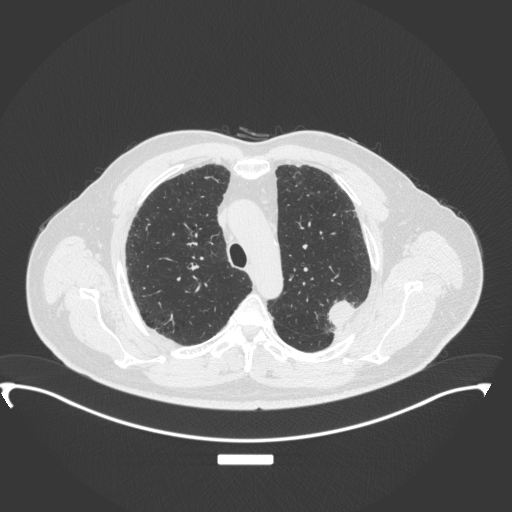
Chest CT, one axial slice; slice 269 of 350 in the series (ordered by position); 120 kVp; lung window (W 1500 / L -600 HU); 1 mm slice thickness; 512 × 512 image matrix, field of view 459 × 459 mm. Male patient, age 64 years. From the clinical record (not read from this slice): clinical TNM (as recorded): T1c N1 M1.
Outlined on this slice (rectangle marked by the reading radiologist):
- lung tumour (recorded histology: adenocarcinoma): bounding box (x1, y1, x2, y2) in pixels: (322, 294, 361, 334)